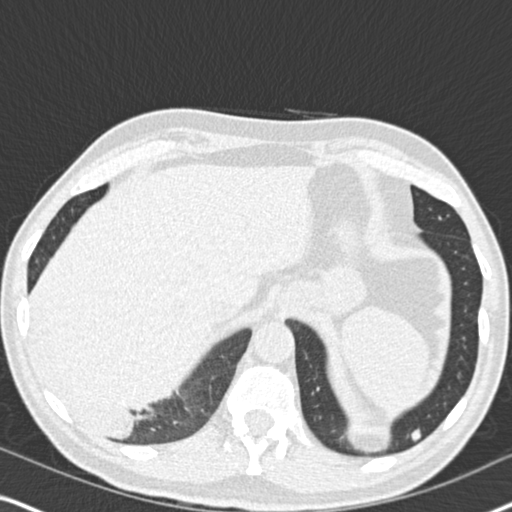
Axial slice from a low-dose chest CT screening exam. Second annual screen. Lung window (W 1500 / L -600 HU). 2 mm slice thickness. 512 × 512 image matrix, field of view 330 × 330 mm. Male participant, aged 61 years at enrolment.
- Expert-annotated lung lesion, bounding box <11,267,178,453> (left, top, right, bottom; pixels).
- Screening reader's record for this exam (one nodule recorded; not confirmed to be the boxed lesion): non-calcified nodule or mass ≥4 mm, right lower lobe, 90 × 80 mm, soft tissue attenuation, pre-existing on the prior screen: yes; interval growth: yes.
- Lung cancer was diagnosed 20 days after this screen: bronchiolo-alveolar adenocarcinoma, NOS, right lower lobe, moderately differentiated (G2), stage IIIB (AJCC 6th edition), 90 mm at pathology.